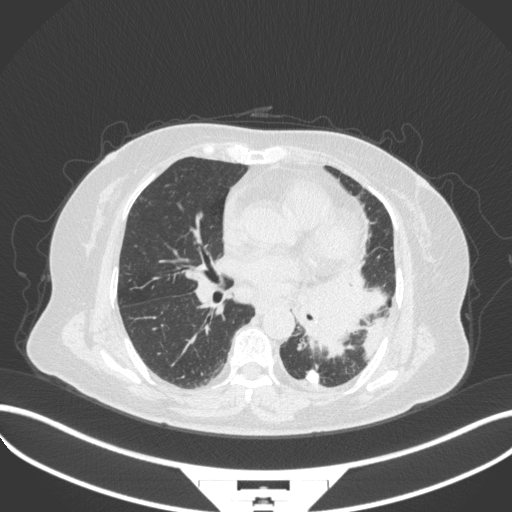
Chest CT, one axial slice; position 169 of 328 along the scan axis; reconstruction kernel B31f; lung window (W 1500 / L -600 HU); 1 mm slice thickness; 512 × 512 image matrix, field of view 400 × 400 mm. Patient: female, 69 years. From the clinical record (not read from this slice): clinical TNM (as recorded): T2b N3 M1.
Structures marked on this image (rectangle marked by the reading radiologist):
- lung tumour (recorded histology: adenocarcinoma): bounding box (x1, y1, x2, y2) in pixels: (291, 279, 390, 356)